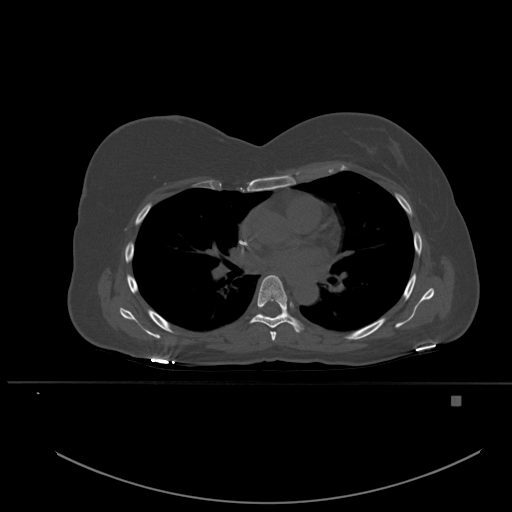
CT including the spine, one axial slice; bone window (W 1800 / L 400 HU); 1.5 mm slice thickness; 512 × 512 image matrix. Patient: female, 49 years. From the clinical record (not read from this slice): primary cancer: breast.
Outlined on this slice (semi-automatic segmentation, software-assisted and operator-edited):
- T5 vertebra: bounding box <270,331,277,341> (left, top, right, bottom; pixels)
- T6 vertebra: <250,275,303,333>